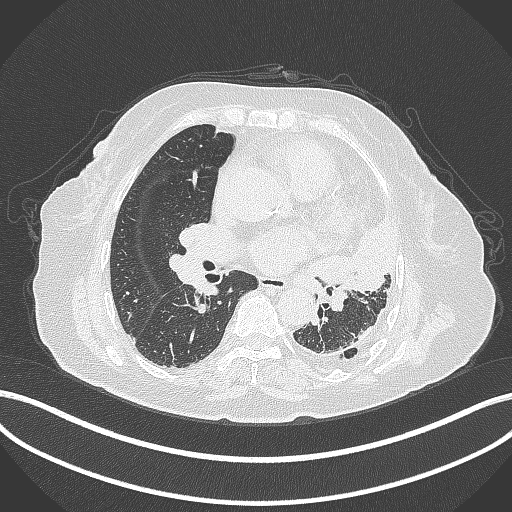
Chest CT, one axial slice. Position 187 of 399 along the scan axis. 120 kVp. Lung window (W 1500 / L -600 HU). 512 × 512 image matrix, field of view 400 × 400 mm. Patient: female, 75 years. Case-level facts recorded for this patient, not image findings: clinical TNM (as recorded): T3 N3 M1.
Structures marked on this image (rectangle marked by the reading radiologist):
- lung tumour (recorded histology: adenocarcinoma): bounding box (x1, y1, x2, y2) in pixels: (318, 212, 399, 301)